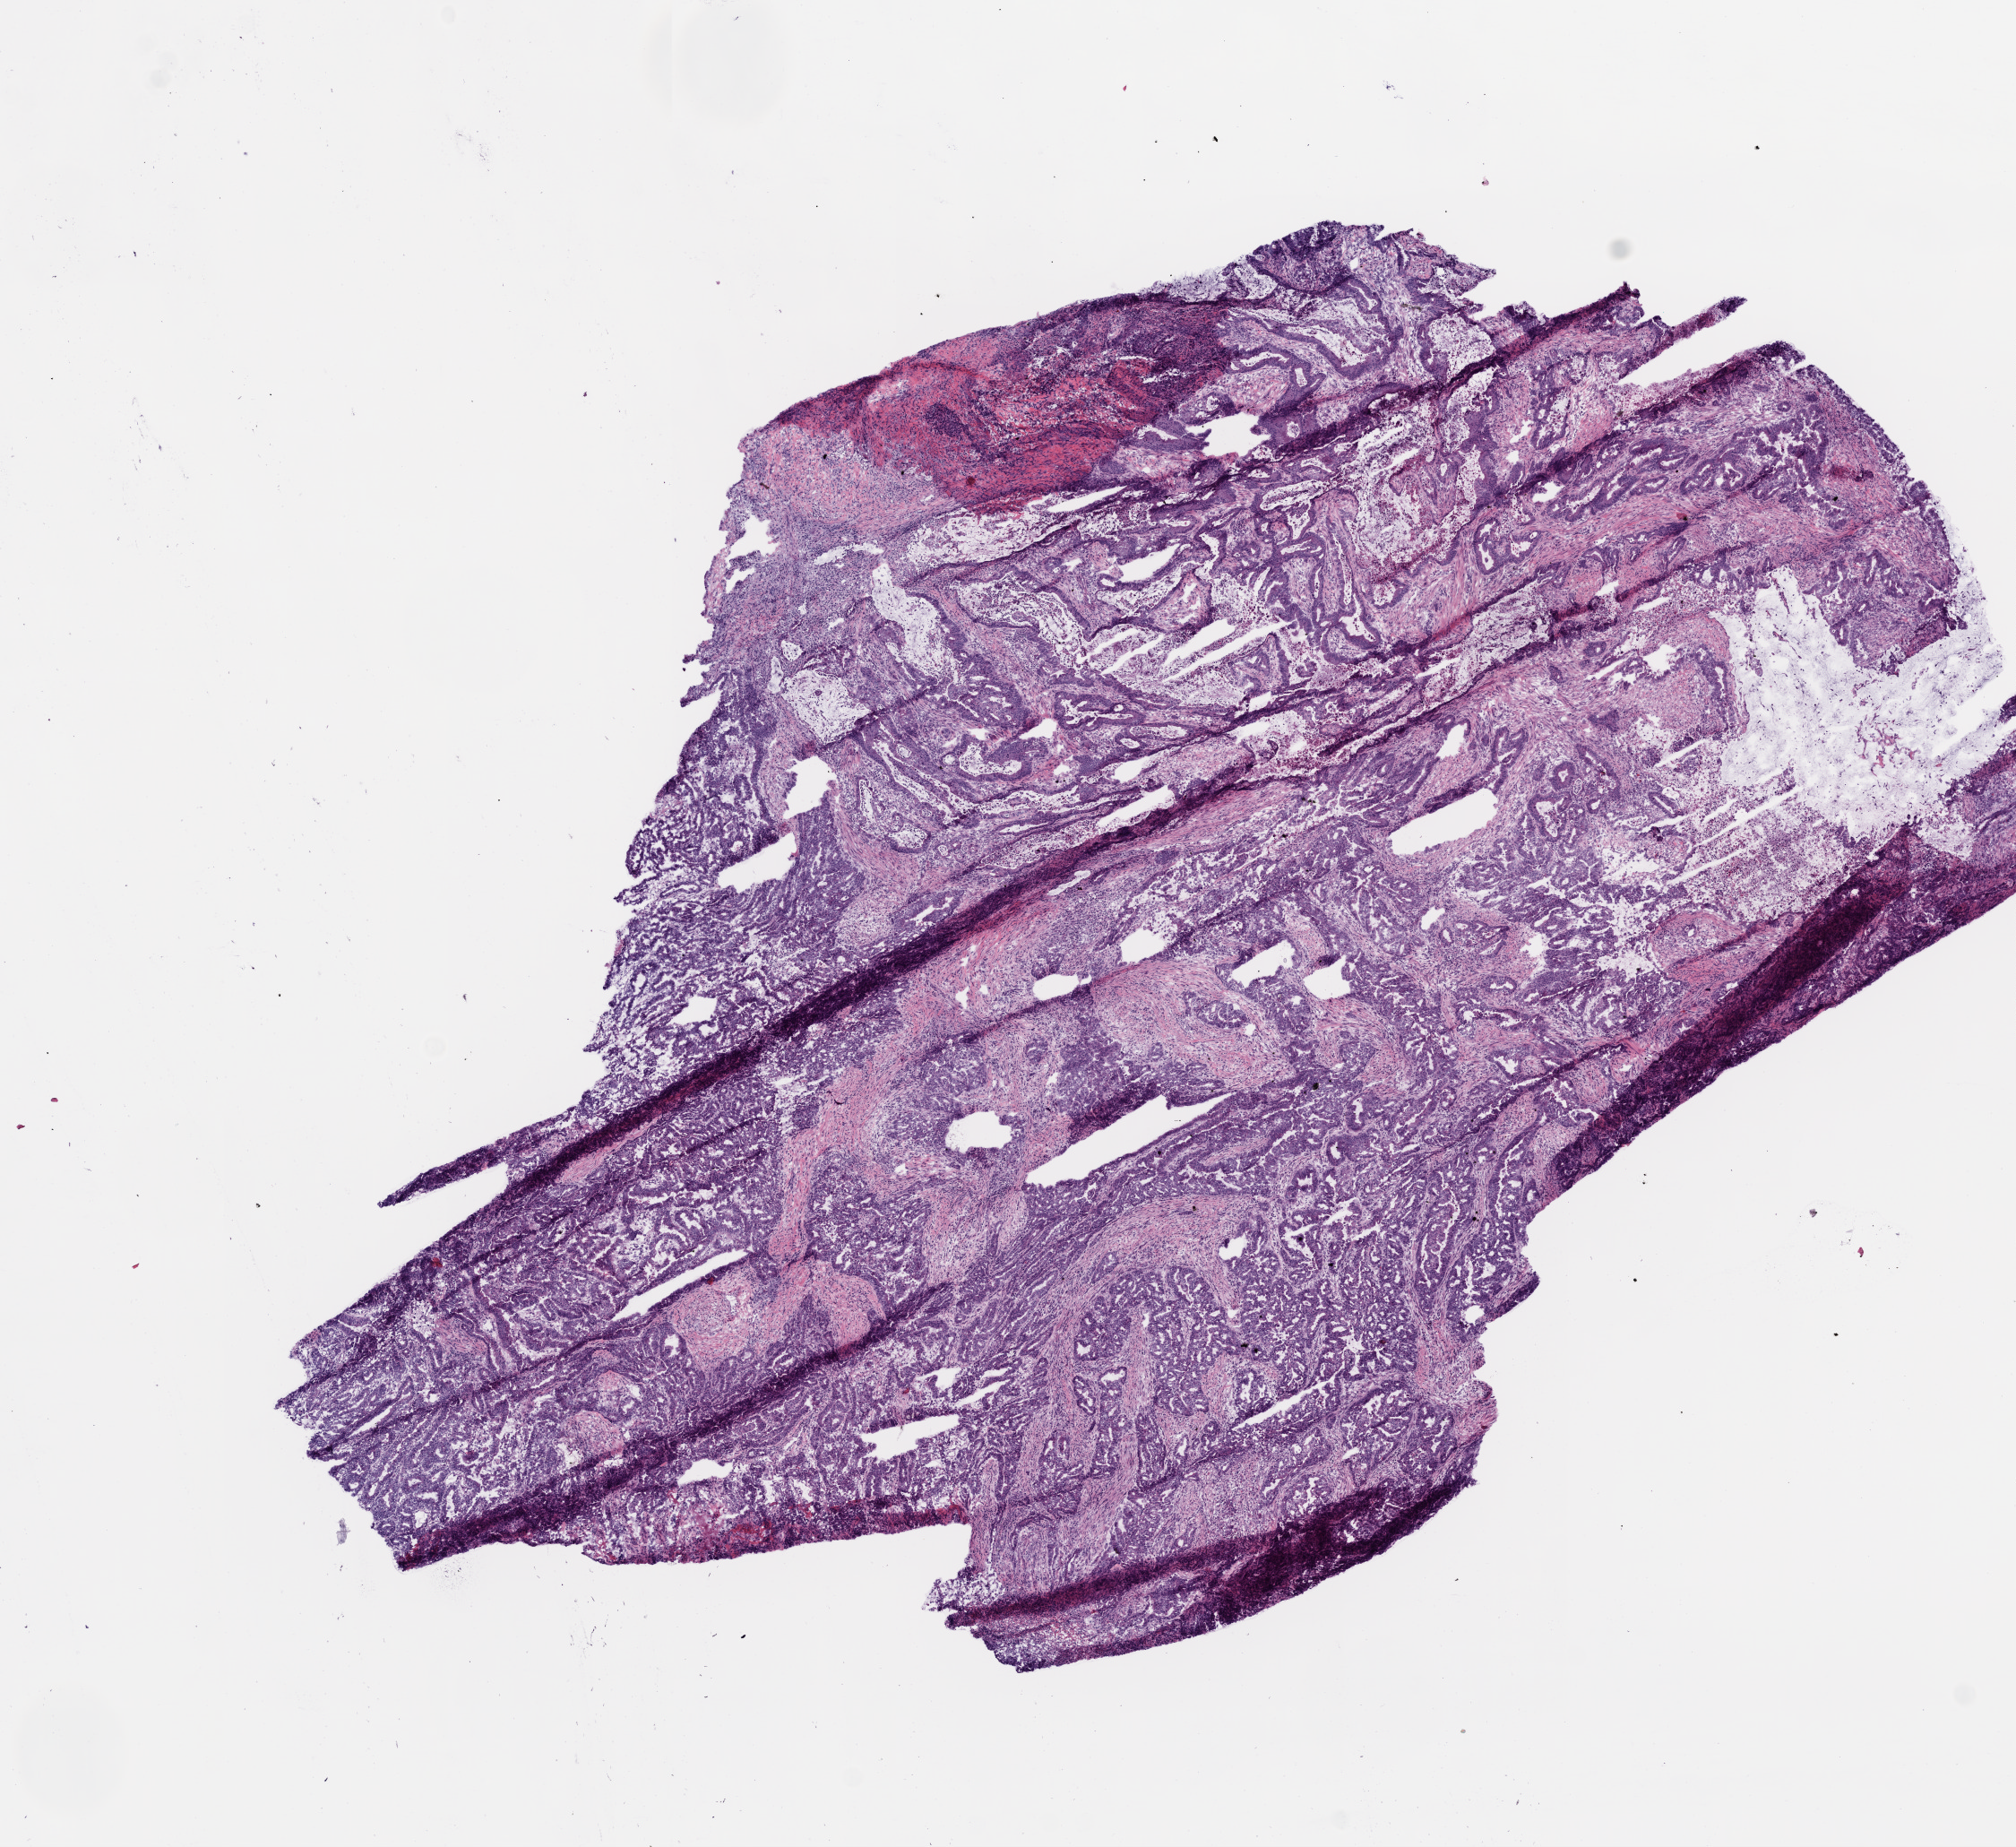
Whole-slide histology image, Hematoxylin and eosin (H&E) stained, shown as a low-resolution overview of the whole scanned area (about 9.0 x 8.3 mm). Frozen section from the bottom of the tissue portion. Sample: primary tumour, stomach. Male patient; age at initial diagnosis 83 years. Histologic grade: G2 (moderately differentiated). Pathologist review of this section (percent, as recorded): tumour cells 70%, tumour nuclei 75%, normal cells 0%, stromal cells 22%, necrosis 8%. Inflammatory infiltration, as recorded: lymphocyte infiltration 8%, neutrophil infiltration 2%.
Lymph nodes positive (case pathology): 14 of 16 examined. Pathologic diagnosis: Adenocarcinoma, intestinal type (body of stomach). AJCC pathologic stage: IIIA (5th edition). TNM: T2 N2 M0.